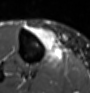
MRI of an extremity soft-tissue mass, one axial slice. Slice 26 of 60 in the series (ordered by position). STIR. MR volume resampled by the dataset authors to the PET/CT grid (not the native acquisition matrix). 3.27 mm slice thickness. 90 × 93 image matrix, field of view 88 × 91 mm. Female patient. From the clinical record (not read from this slice): histological type: undifferentiated – high grade; grade: high; site of the primary tumour: right thigh.
Outlined on this slice (expert contour drawn on MRI and transferred to this co-registered scan by the dataset authors):
- gross tumour volume (mass): bounding box [x1, y1, x2, y2] px = [31, 26, 63, 63]